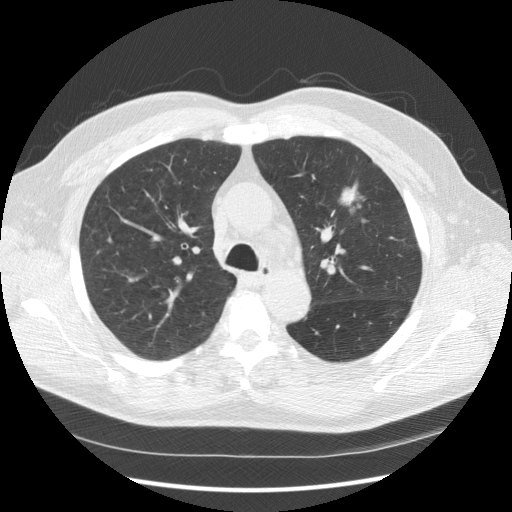
Chest CT (low-dose screening protocol), one axial image. Second annual screen. Lung window (W 1500 / L -600 HU). 2.5 mm slice thickness. Standard (soft-tissue) reconstruction kernel (STANDARD). Slice 50 of 157 in the series. 512 × 512 image matrix. Male participant, aged 65 years at enrolment. Current smoker at enrolment.
• Expert reader's lesion annotation, bounding box <326,173,375,225> (left, top, right, bottom; pixels).
• The screening reader recorded 2 non-calcified nodules or masses ≥4 mm on this exam (left upper lobe, right upper lobe); which of them this box marks is not recorded.
• Official screen result: positive, other.
• Lung cancer was diagnosed 120 days after this screen: carcinoma, NOS, left upper lobe, poorly differentiated (G3), stage IIIA (AJCC 6th edition), 25 mm at pathology.